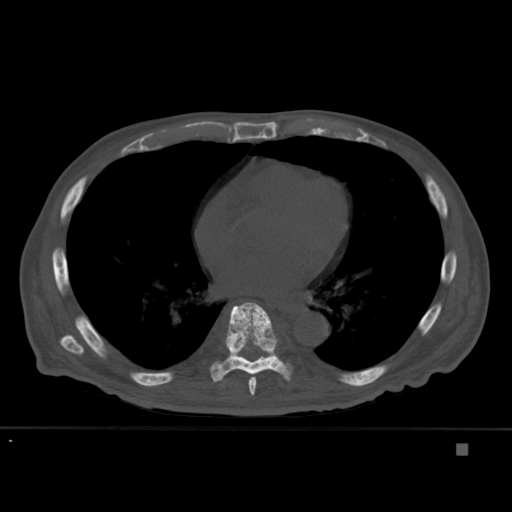
CT including the spine, one axial slice; slice 265 of 451 in the series (ordered by position); bone window (W 1800 / L 400 HU); 512 × 512 image matrix, field of view 378 × 378 mm. Patient: male, 75 years. Case-level facts recorded for this patient, not image findings: primary cancer: prostate.
Annotated regions visible in this slice (semi-automatically segmented with operator editing):
- T7 vertebra: box from (x=248, y=377) to (x=257, y=396) px
- T8 vertebra: (x=210, y=302)–(x=293, y=383)
- T9 vertebra: (x=262, y=356)–(x=269, y=358)